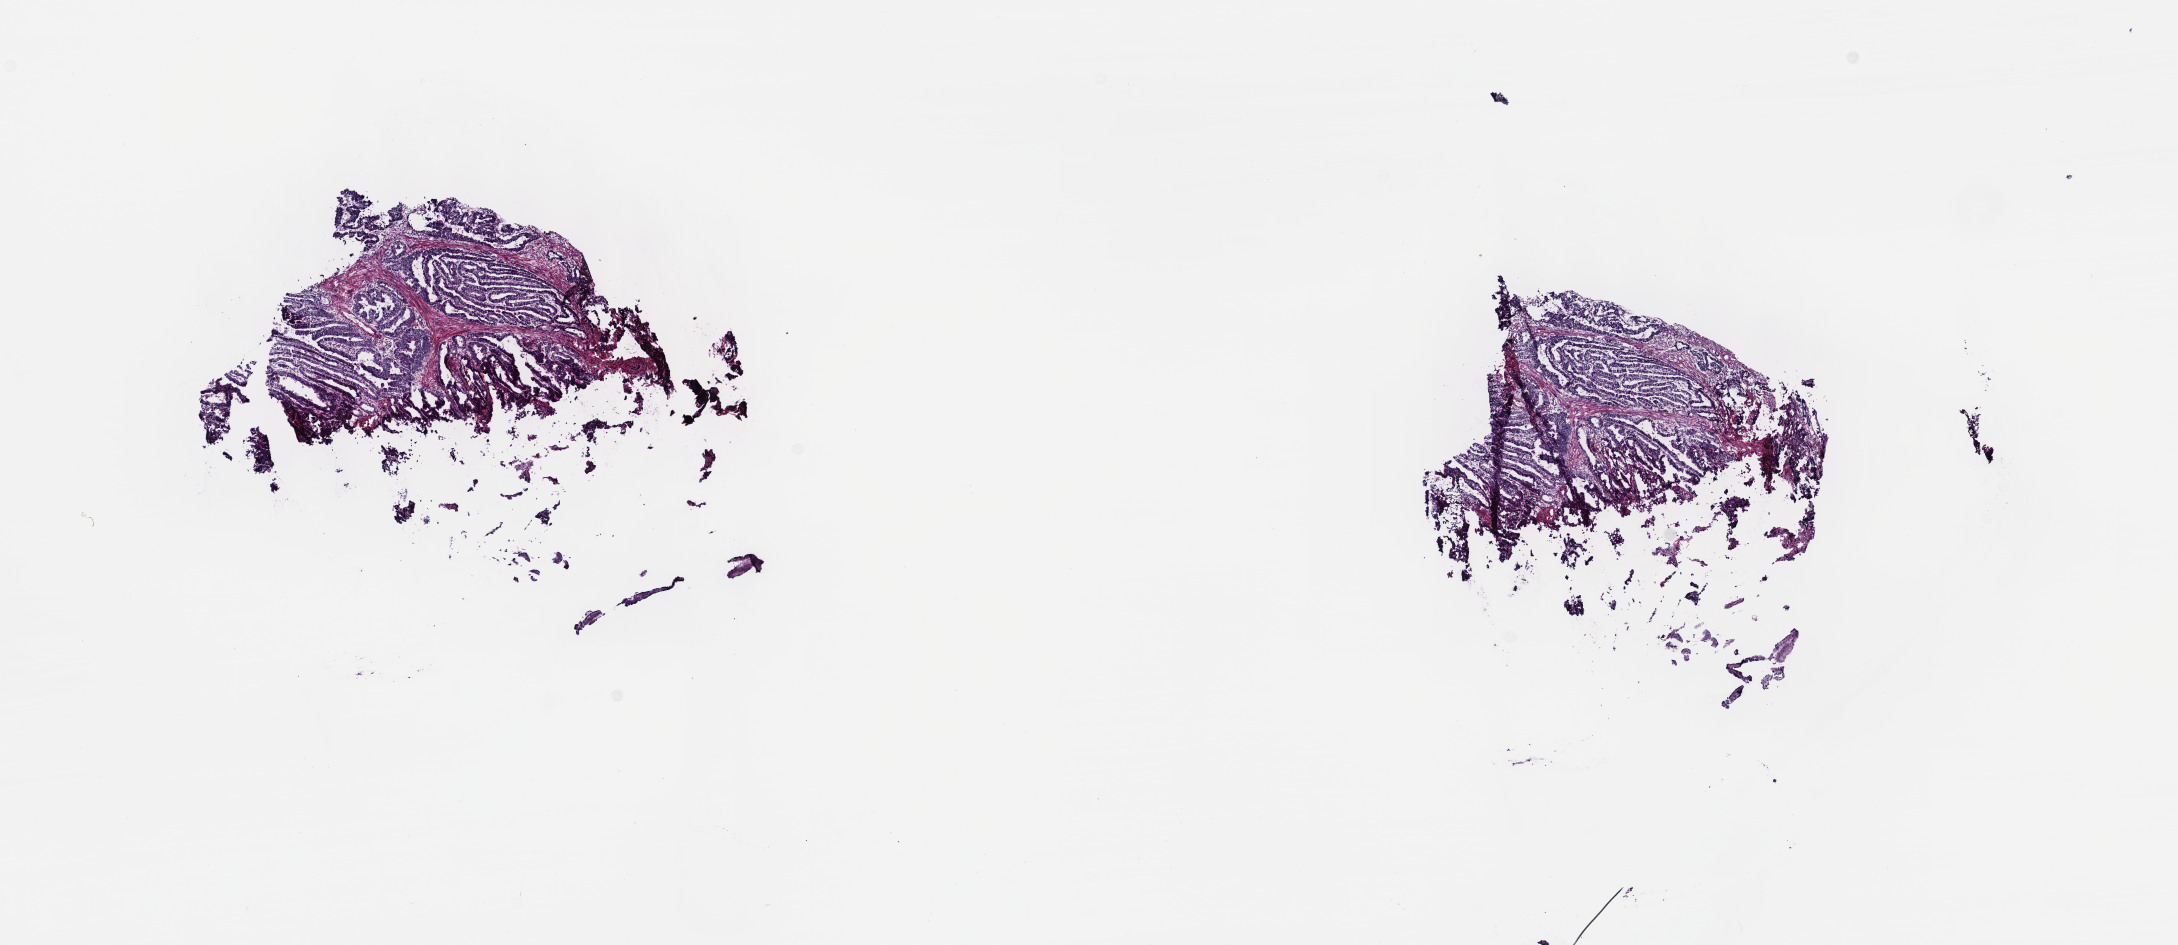
Whole-slide histology image, H&E-stained, a low-resolution overview of the entire scanned area, about 17.6 x 7.6 mm. Frozen section from the top of the tissue portion. Sample: primary tumour, stomach. Male patient; age at initial diagnosis 63 years.
Diagnosis: Tubular adenocarcinoma (gastric antrum).